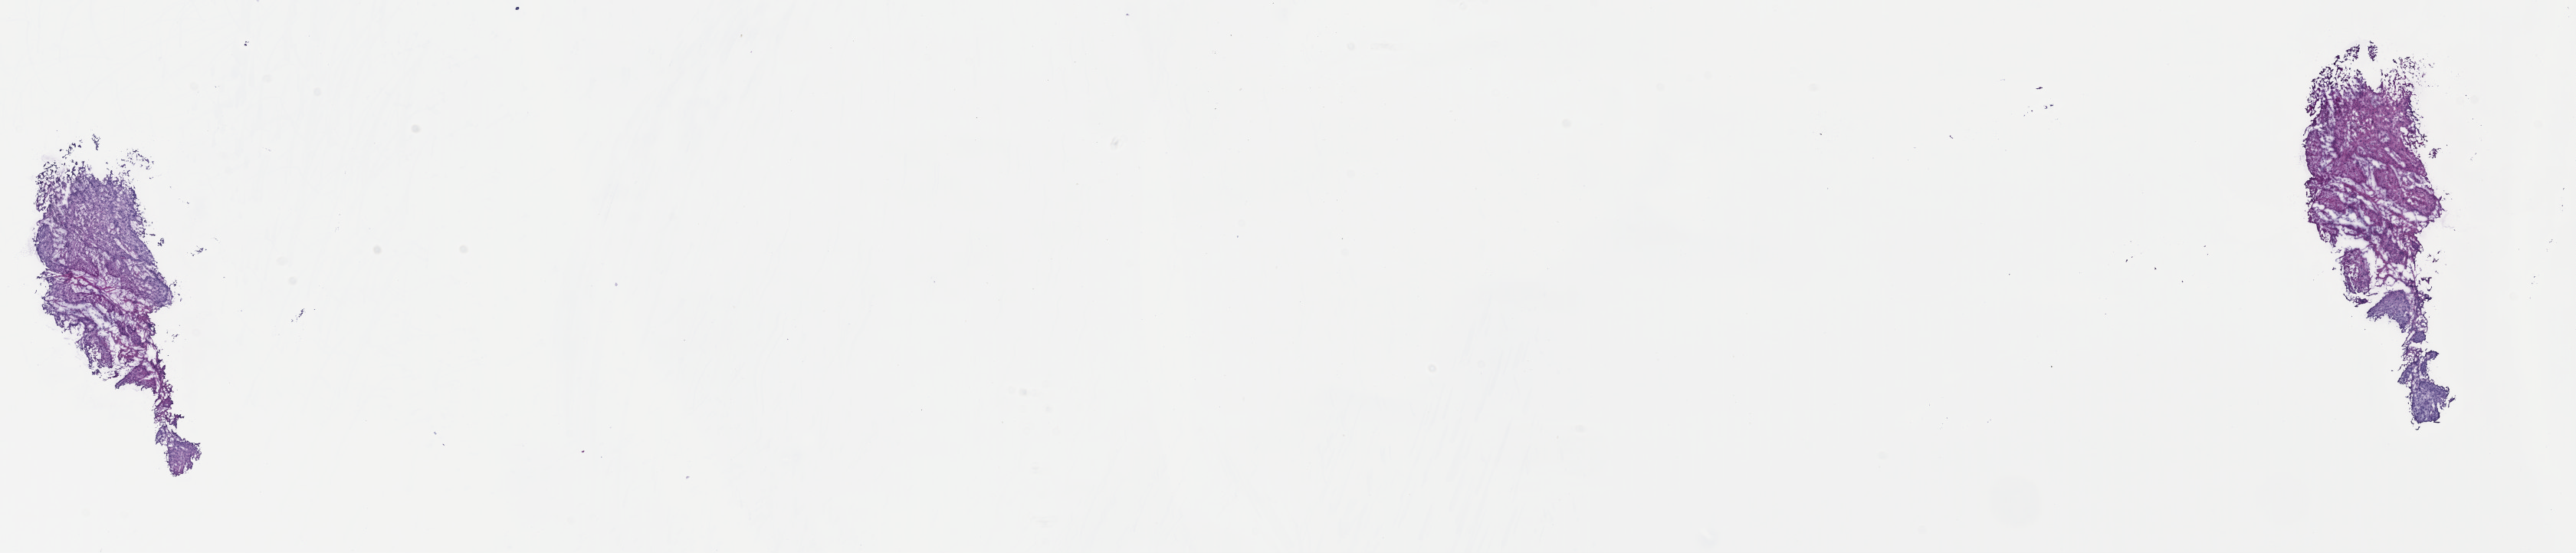
Whole-slide histology image, H&E-stained, shown as a low-resolution overview of the whole scanned area (about 26.4 x 5.7 mm), frozen section from the top of the tissue portion, sample: primary tumour, head and neck. Patient: male, age at initial diagnosis 79 years. Histologic grade: G1 (well differentiated). Composition of this section per pathologist review: tumour cells 80%, tumour nuclei 60%, normal cells 0%, stromal cells 20%, necrosis 0%. Inflammatory infiltration, as recorded: lymphocyte infiltration 0%, monocyte infiltration 0%, neutrophil infiltration 30%.
Diagnosis: Squamous cell carcinoma, NOS (mouth, NOS). AJCC pathologic stage: IVA. Lymph nodes positive (case pathology): 0 of 49 examined.